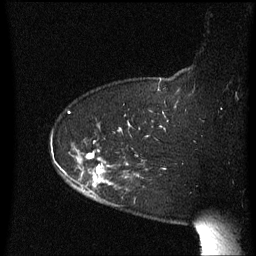
Breast MRI (dynamic contrast-enhanced), one sagittal slice; slice 50 of 60 in the series (ordered by position); dynamic contrast-enhanced series, image 2 of 3 at this slice position (ordered by acquisition); 1.5 T; TE 4.2 ms, TR 8.4 ms; 2.3 mm slice thickness; 256 × 256 image matrix, field of view 200 × 200 mm. Patient: female, 63 years. From the clinical record (not read from this slice): setting: breast cancer imaged before/during neoadjuvant chemotherapy; receptor status: HER2-positive.
Outlined on this slice (semi-automatic segmentation, software-assisted and operator-edited):
- analysis volume of interest (the breast-tissue region the enhancement analysis was run in; not a lesion): box from (x=63, y=144) to (x=143, y=205) px
- tumour enhancement mask (voxels above the 70 % enhancement threshold inside the analysis volume of interest): (x=87, y=153)–(x=104, y=183)